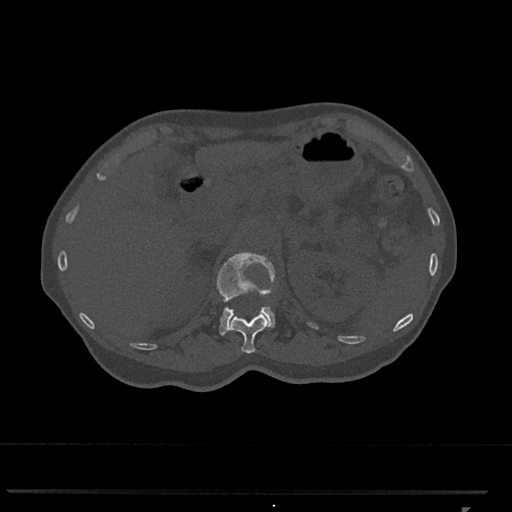
CT including the spine, one axial slice. Position 433 of 793 along the scan axis. Reconstruction kernel Br40s/3. 120 kVp. Bone window (W 1800 / L 400 HU). 0.5 mm slice thickness. 512 × 512 image matrix, field of view 380 × 380 mm. Female patient, age 62 years. From the clinical record (not read from this slice): primary cancer: renal.
Annotated regions visible in this slice (semi-automatic segmentation, software-assisted and operator-edited):
- L1 vertebra: box from (x=217, y=252) to (x=275, y=335) px
- T12 vertebra: (x=229, y=313)–(x=268, y=354)